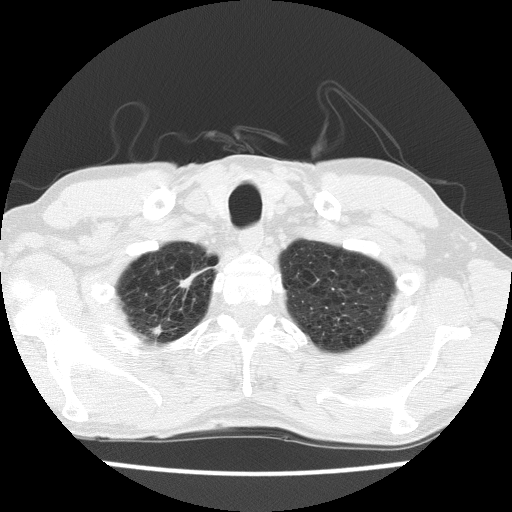
Axial slice from a low-dose chest CT screening exam; second annual screen; lung window (W 1500 / L -600 HU); 2 mm slice thickness; slice 16 of 175 in the series; 512 × 512 image matrix. Male participant, aged 63 years at enrolment. Current smoker at enrolment.
- Expert reader's lesion annotation, bounding box [x1, y1, x2, y2] px = [137, 264, 208, 333].
- Screening reader's record for this exam: no non-calcified nodule ≥4 mm recorded.
- Participant outcome: lung cancer diagnosed 390 days after this screen — adenocarcinoma, NOS, right upper lobe, moderately differentiated (G2), stage IIIB (AJCC 6th edition), 17 mm at pathology.